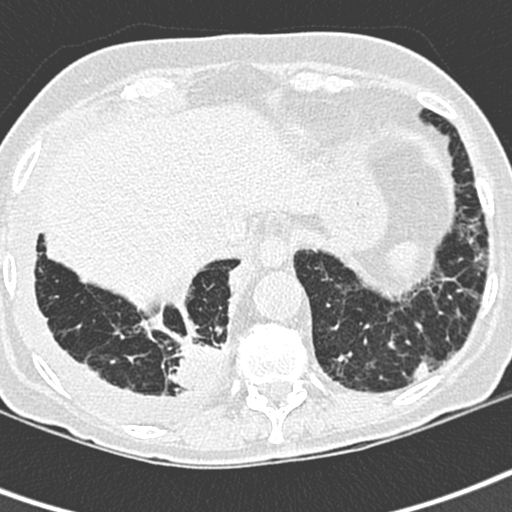
Low-dose screening chest CT, one axial slice; 120 kVp; lung window (W 1500 / L -600 HU); 1.3 mm slice thickness; 512 × 512 image matrix.
Outlined on this slice (manually delineated by an expert):
- lesion 1 (tumor, lower lobe of right lung): bounding box (x1, y1, x2, y2) in pixels: (169, 335, 221, 392)
- lesion 2 (nodule, lower lobe of left lung): (414, 363, 431, 377)